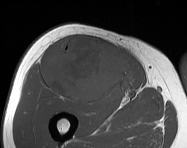
MRI of an extremity soft-tissue mass, one axial slice. Position 84 of 114 along the scan axis. MR volume resampled by the dataset authors to the PET/CT grid (not the native acquisition matrix). 3.27 mm slice thickness. 187 × 148 image matrix. Male patient. Case-level facts recorded for this patient, not image findings: histological type: pleiomorphic leiomyosarcoma; grade: intermediate; site of the primary tumour: right thigh.
Annotated regions visible in this slice (expert contour drawn on MRI and transferred to this co-registered scan by the dataset authors):
- gross tumour volume including surrounding oedema: bounding box <43,36,133,103> (left, top, right, bottom; pixels)
- gross tumour volume (mass): <43,36,133,103>